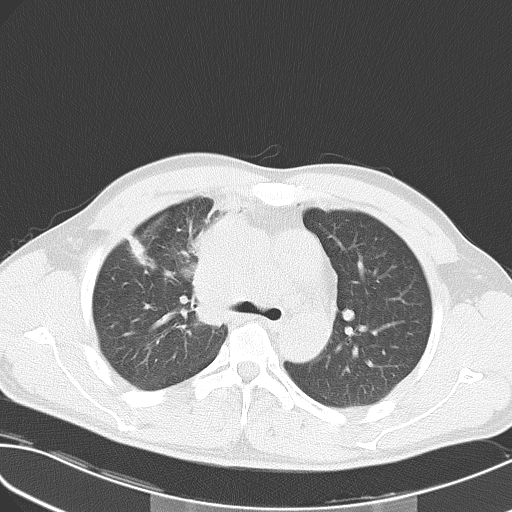
Chest CT, one axial slice; slice 38 of 55 in the series (ordered by position); reconstruction kernel B70f; 120 kVp; lung window (W 1500 / L -600 HU); 512 × 512 image matrix, field of view 346 × 346 mm. Male patient, age 32 years. From the clinical record (not read from this slice): clinical TNM (as recorded): T4 N3 M0; histopathological grade: G3.
Outlined on this slice (rectangle marked by the reading radiologist):
- lung tumour (recorded histology: small cell carcinoma): box from (x=186, y=214) to (x=234, y=336) px